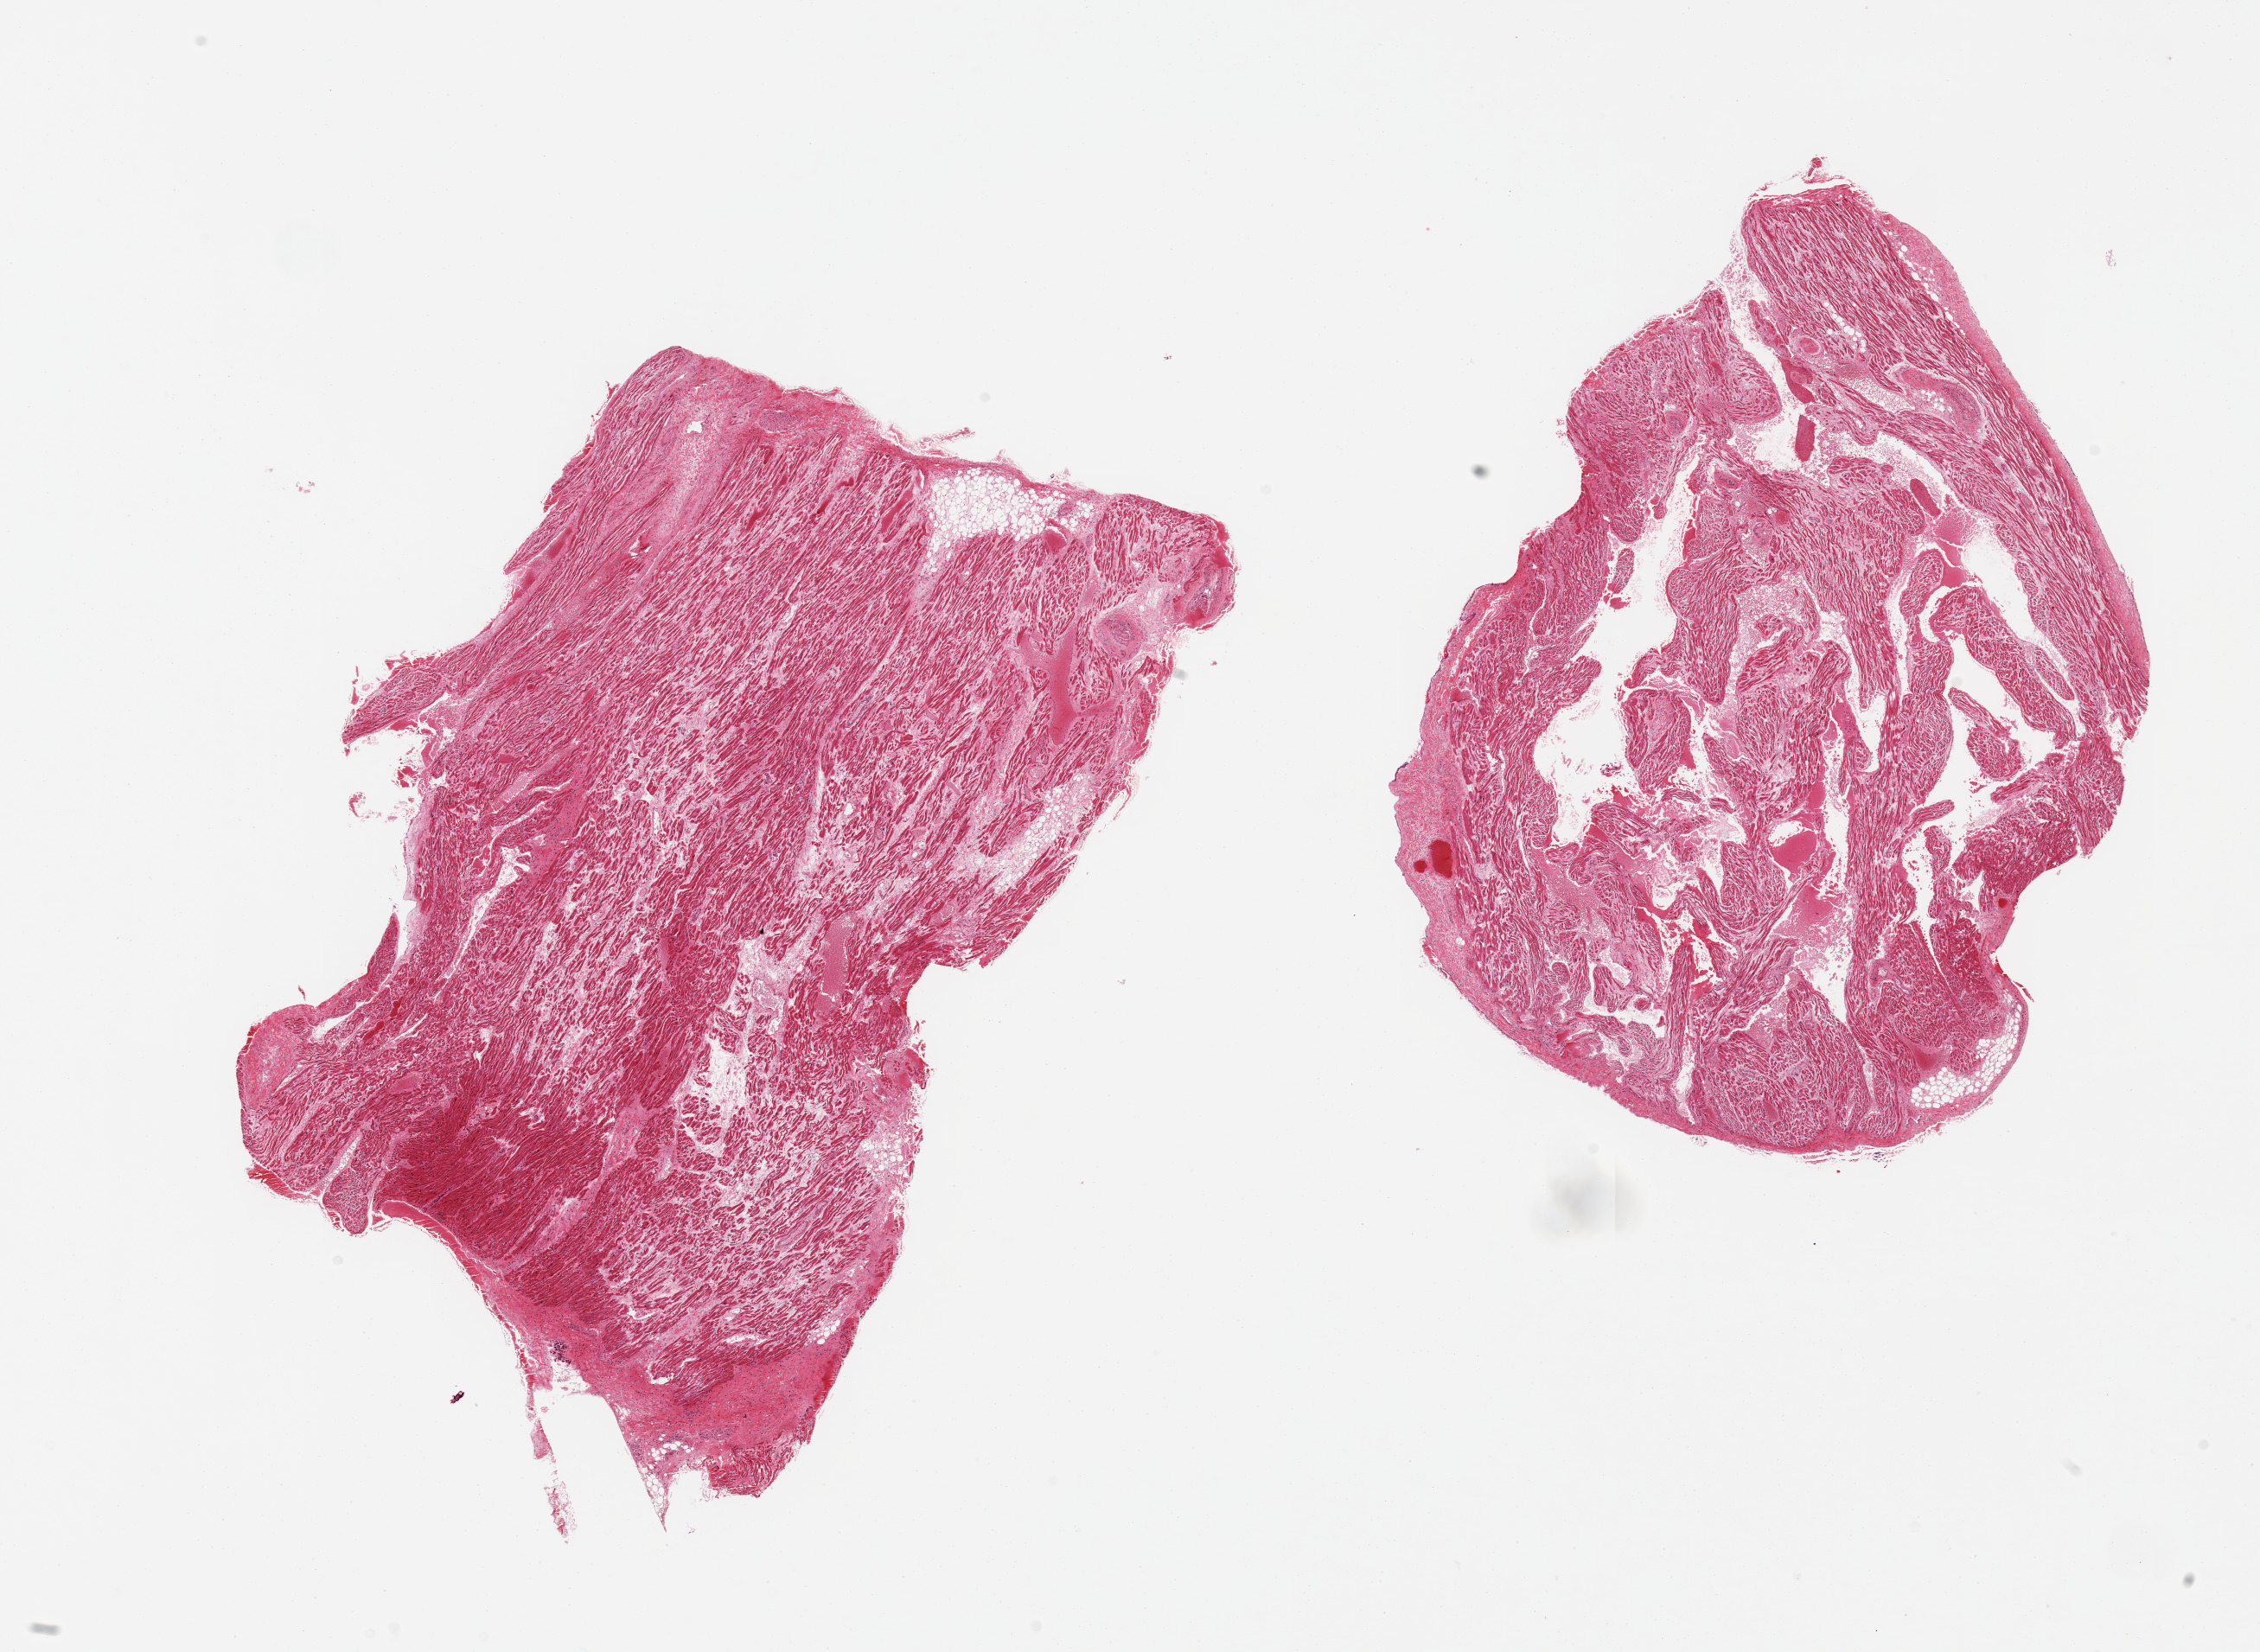
Haematoxylin and eosin whole-slide image, brightfield — whole scanned area (about 20.7 x 15.1 mm, acquisition: 20x scan) shown as a low-resolution overview, PAXgene-fixed paraffin-embedded (PFPE) section, target tissue: auricular appendage, tissue donor sample. Female donor.
Review note (as recorded): 2 pieces, no abnormalities.